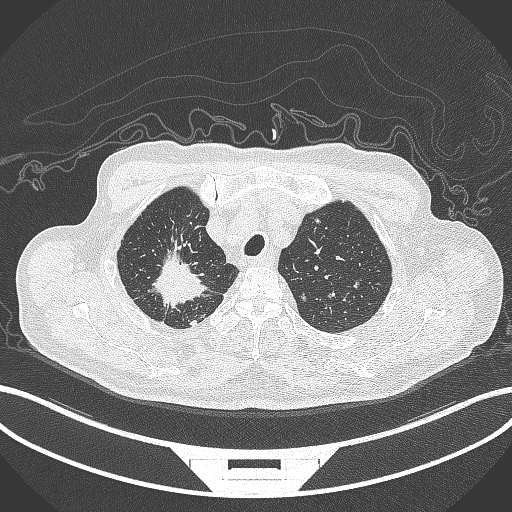
Chest CT, one axial slice; slice 323 of 407 in the series (ordered by position); reconstruction kernel B70f; lung window (W 1500 / L -600 HU); 1 mm slice thickness; 512 × 512 image matrix, field of view 400 × 400 mm. Patient: male, 69 years. Case-level facts recorded for this patient, not image findings: clinical TNM (as recorded): T1c N1 M1.
Outlined on this slice (bounding box drawn by a radiologist):
- lung tumour (recorded histology: adenocarcinoma): box from (x=137, y=242) to (x=211, y=313) px